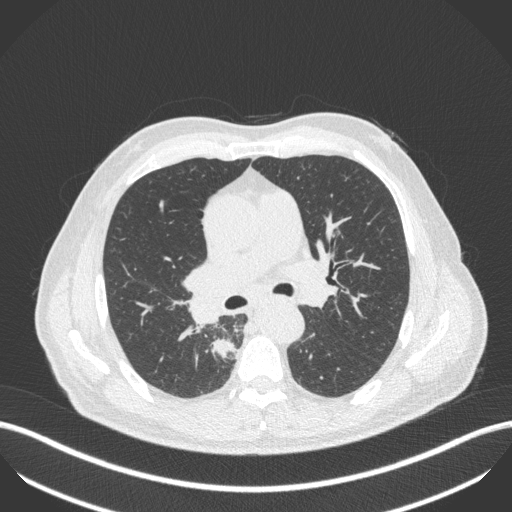
Chest CT, one axial slice. Position 281 of 451 along the scan axis. Lung window (W 1500 / L -600 HU). 1 mm slice thickness. 512 × 512 image matrix, field of view 400 × 400 mm. Patient: male, 61 years. Case-level facts recorded for this patient, not image findings: clinical TNM (as recorded): T1 N0 M0; histopathological grade: G3.
Outlined on this slice (bounding box drawn by a radiologist):
- lung tumour (recorded histology: small cell carcinoma): bounding box <209,336,243,364> (left, top, right, bottom; pixels)